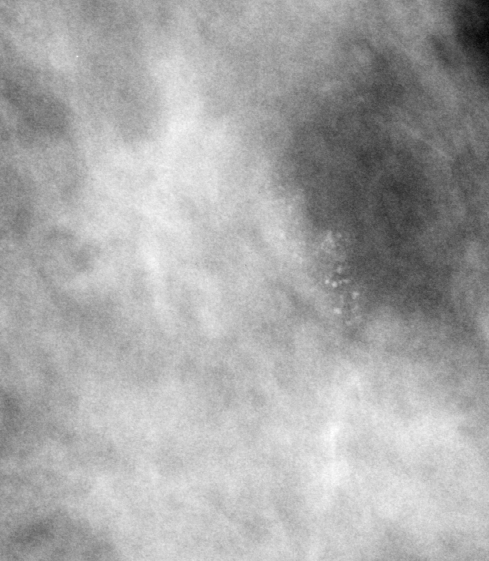
Cropped region of a digitized screen-film mammogram centred on a radiologist-marked abnormality, left breast, MLO view.
- Finding: calcifications, morphology pleomorphic, distribution clustered; BI-RADS assessment category 5; pathology (as recorded): malignant.